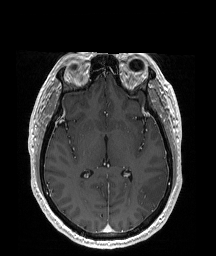
Brain MRI from a brain-tumour surgery series, one axial slice; position 101 of 192 along the scan axis; T1-weighted post-contrast; 1 mm slice thickness; 216 × 256 image matrix, field of view 219 × 260 mm. From the clinical record (not read from this slice): histopathology: Glioblastoma; WHO grade: 4; IDH mutation: no; tumour location: Left Temporal Parietal.
Outlined on this slice (manually delineated by an expert):
- tumour: bounding box <140,175,168,206> (left, top, right, bottom; pixels)